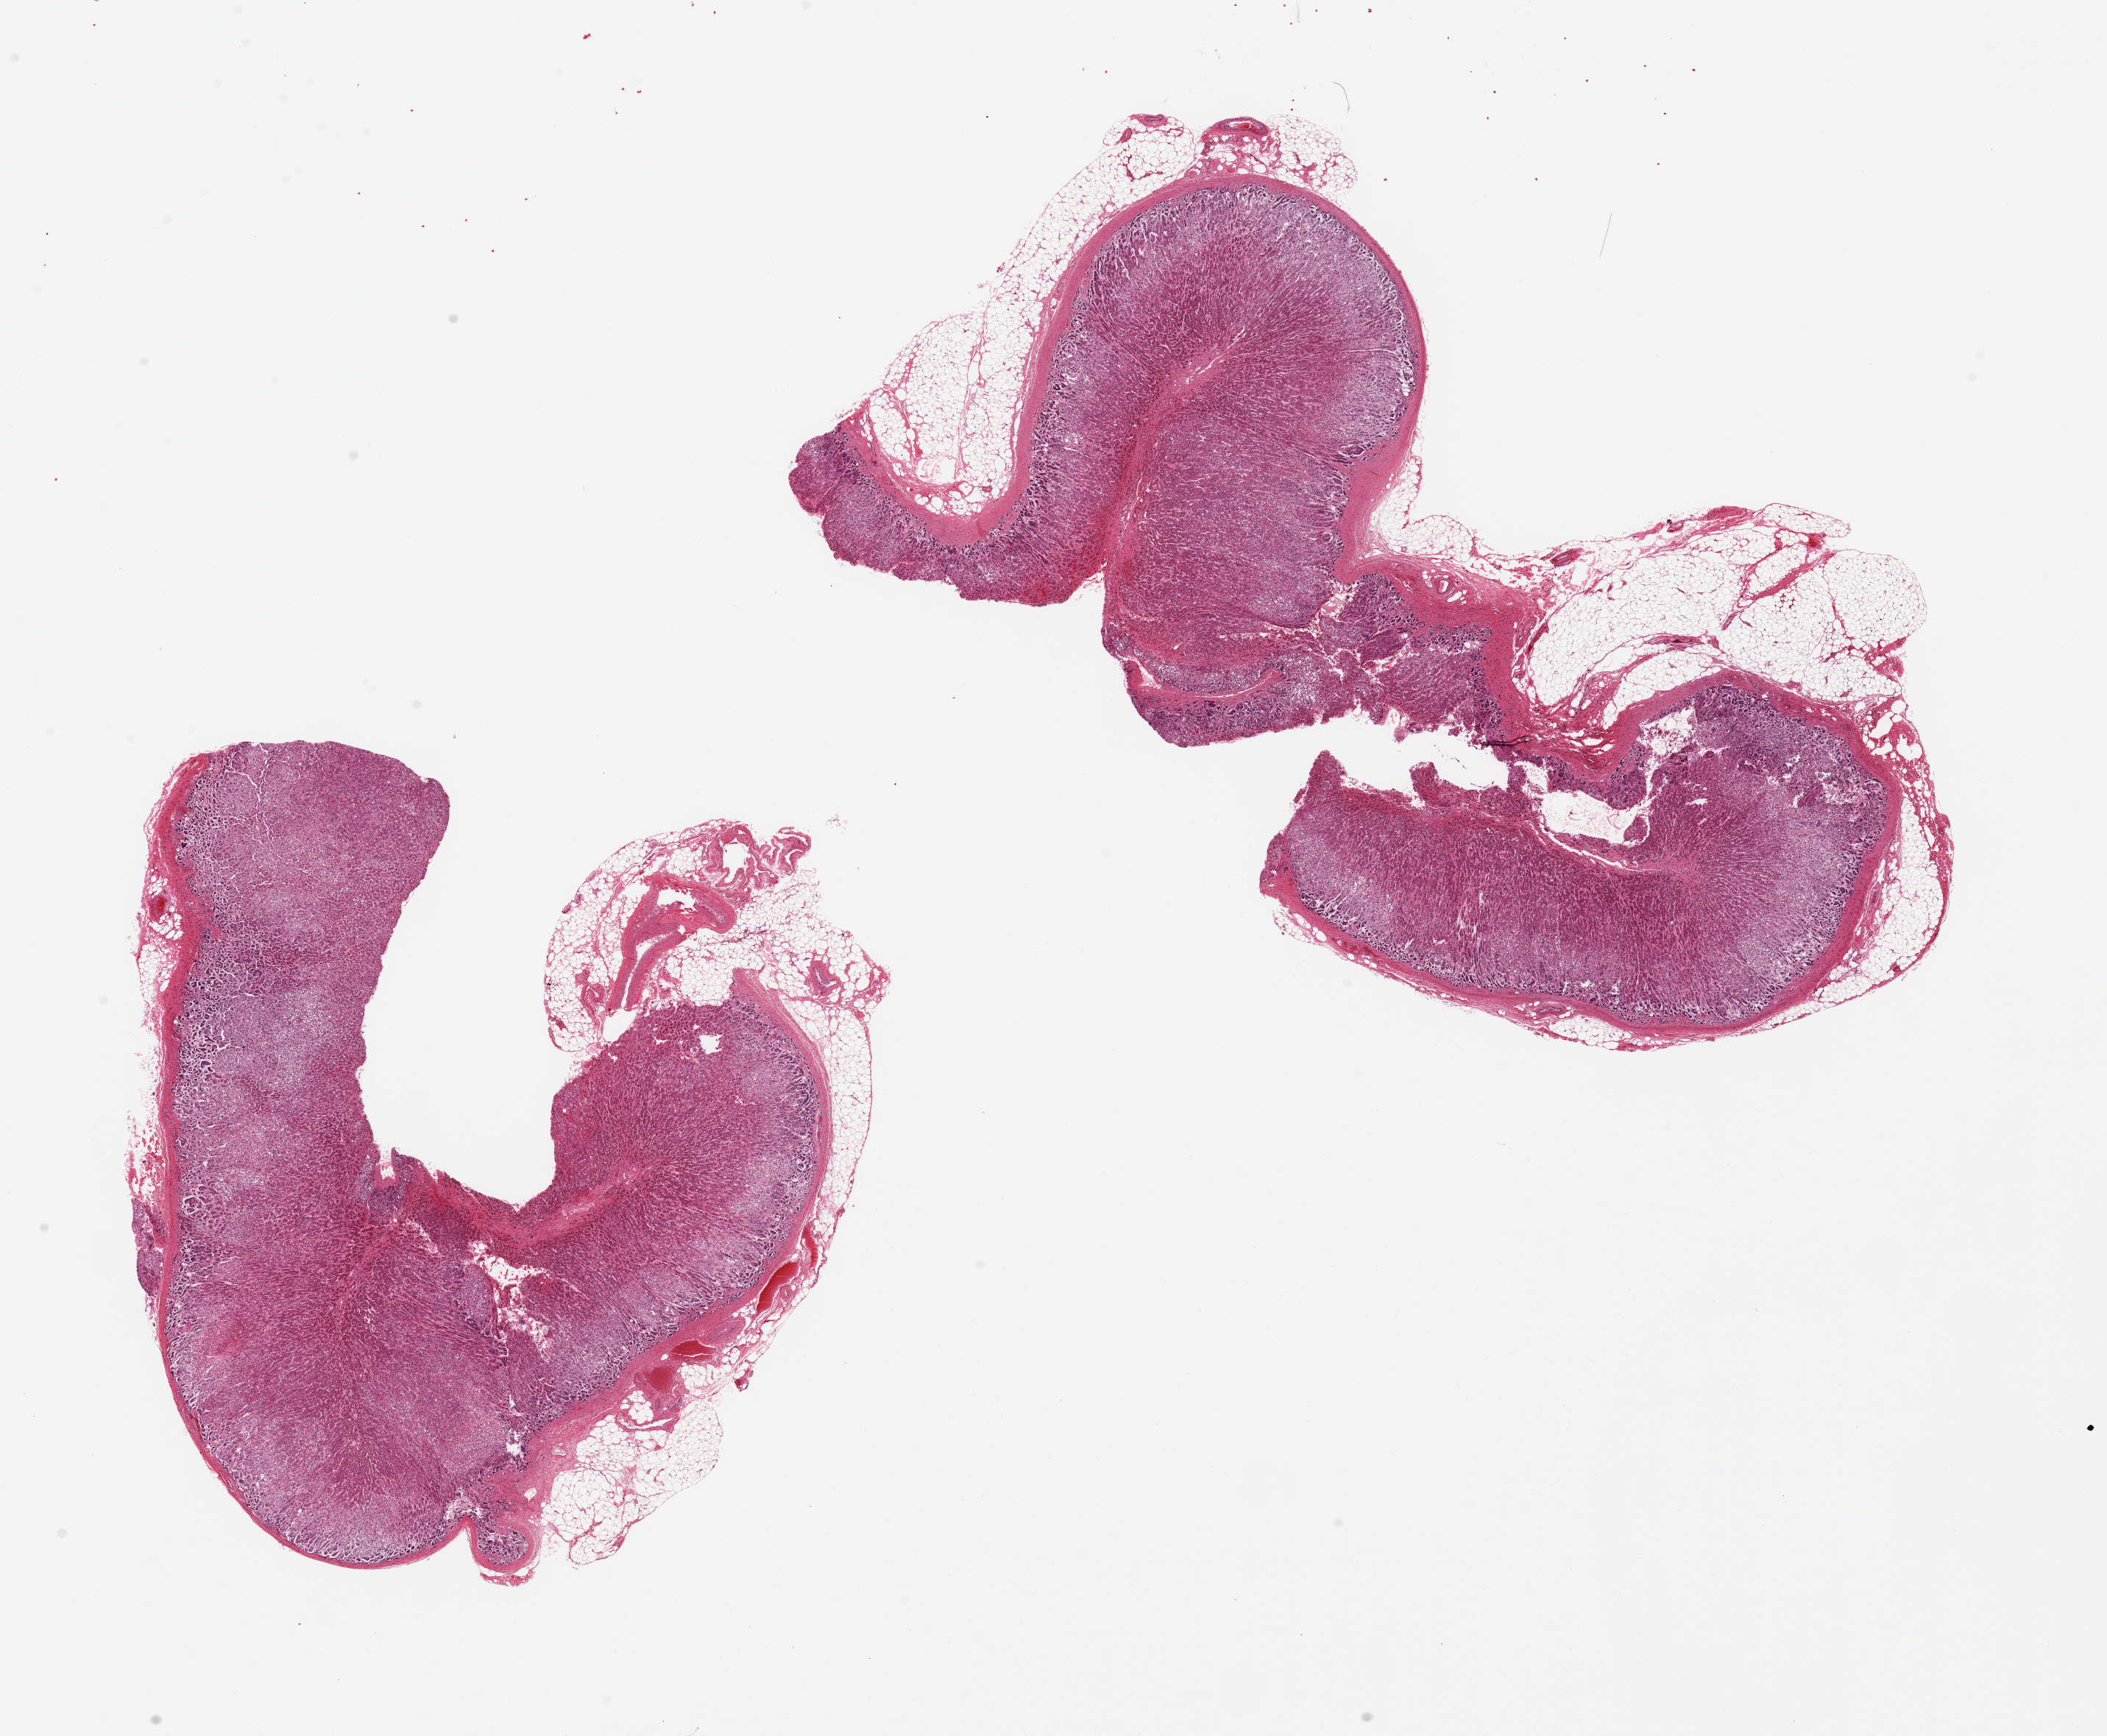
Whole-slide image, hematoxylin and eosin (H&E) stain — low-resolution overview of the scanned area, about 22.6 x 18.7 mm; PAXgene-fixed, paraffin-embedded tissue; section of adrenal gland (target tissue); tissue donor sample. Donor: male.
Pathologist's review note for this sample: 2 pieces 11x6 & 9x9 mm;~ 20-30% peripheral adipose; largely cortex.